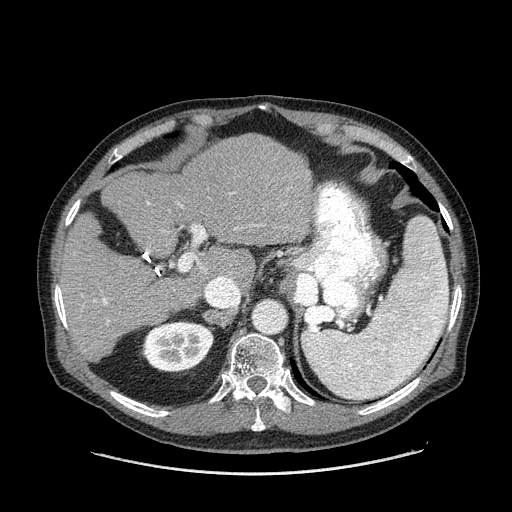
Contrast-enhanced abdominal CT (liver protocol), one axial slice; position 96 of 180 along the scan axis; 120 kVp; one of 2 acquisitions stored at this slice position; soft-tissue window (W 400 / L 40 HU); 2.5 mm slice thickness; 512 × 512 image matrix, field of view 420 × 420 mm. From the clinical record (not read from this slice): diagnosis: hepatocellular carcinoma (patient treated with transarterial chemoembolisation; whether this scan precedes or follows treatment is not stated here); TNM stage (as recorded): Stage-II; Child-Pugh class: A; tumour nodularity: multinodular; tumour size: 2.8 cm.
Structures marked on this image (semi-automatically segmented with operator editing):
- liver parenchyma outside the tumour (the mass and vessels are separate outlines, so this box may not span the whole liver): bounding box [x1, y1, x2, y2] px = [59, 134, 314, 362]
- liver vessels: [94, 193, 286, 323]